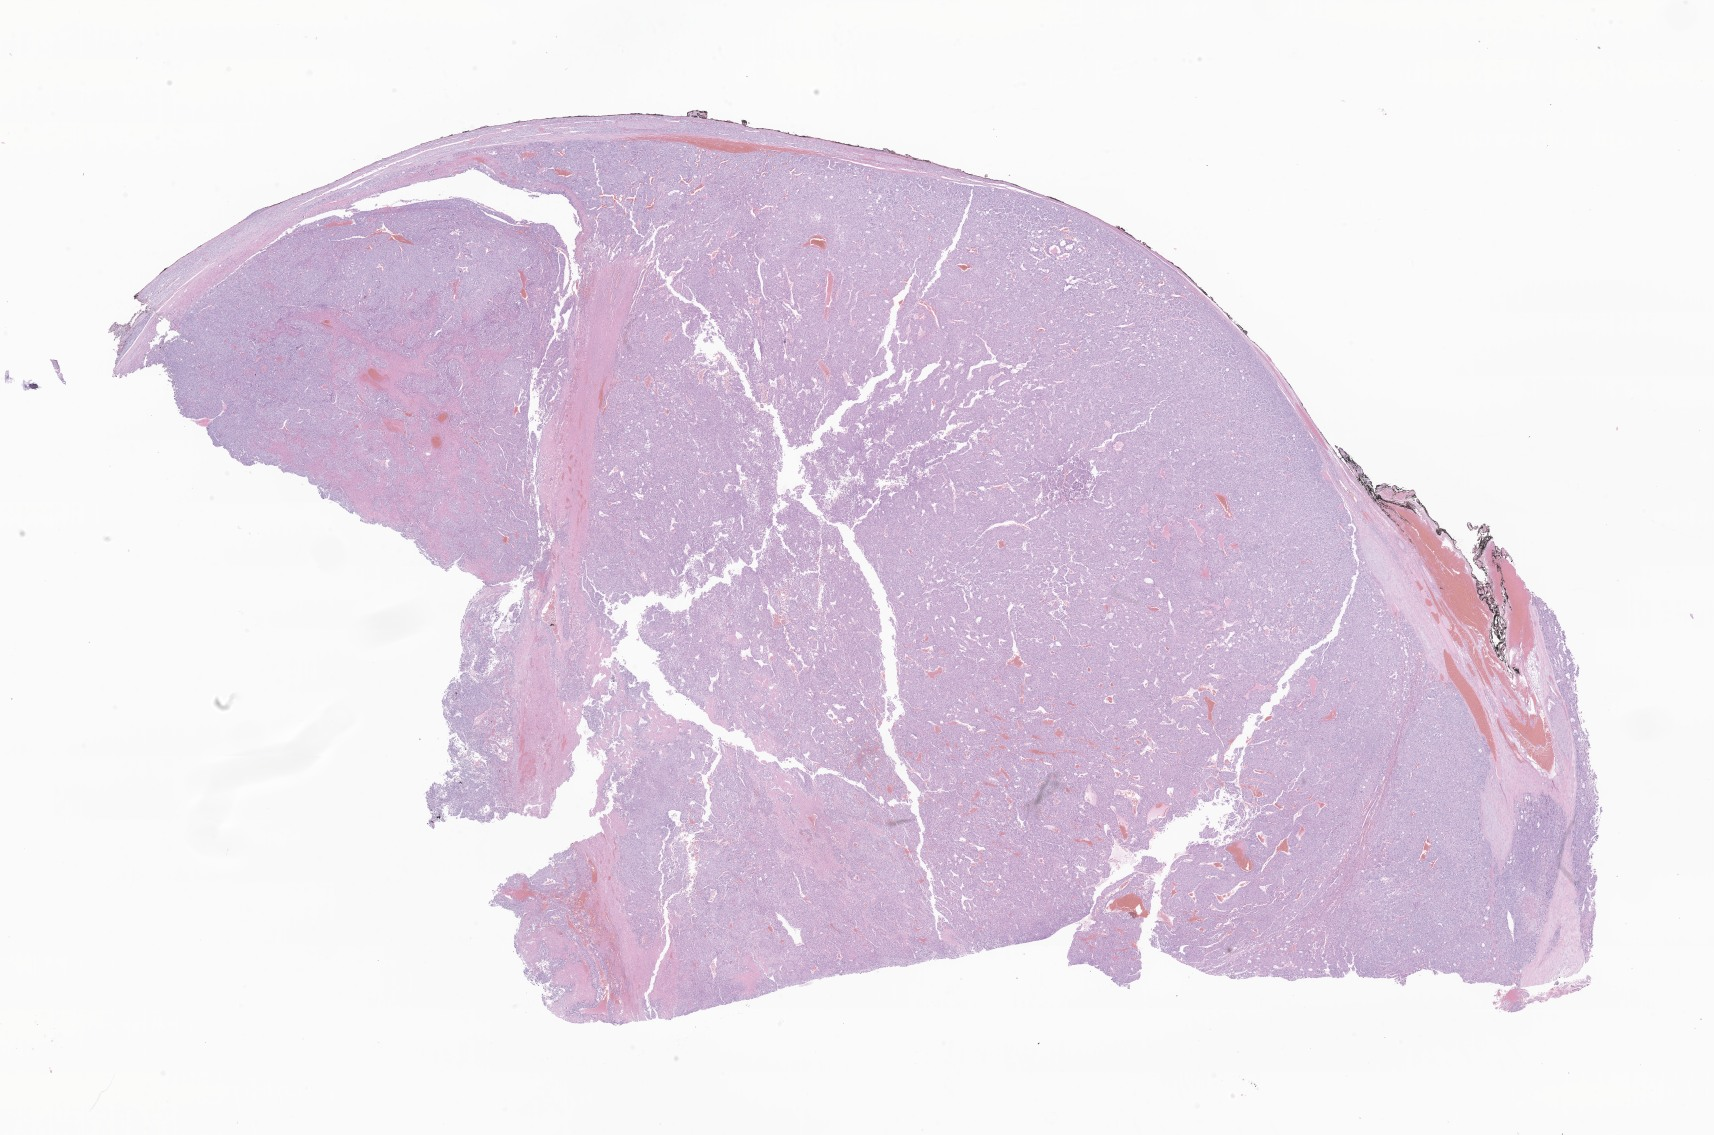
Whole-slide image, haematoxylin and eosin stain of tumor tissue from the adrenal gland, a low-resolution overview of the entire scanned area, about 28.9 x 19.1 mm. Formalin-fixed paraffin-embedded section. Patient: male, age 882 days (about 2.4 years).
Diagnosis (ICD-O-3 morphology term): Adrenal cortical carcinoma.